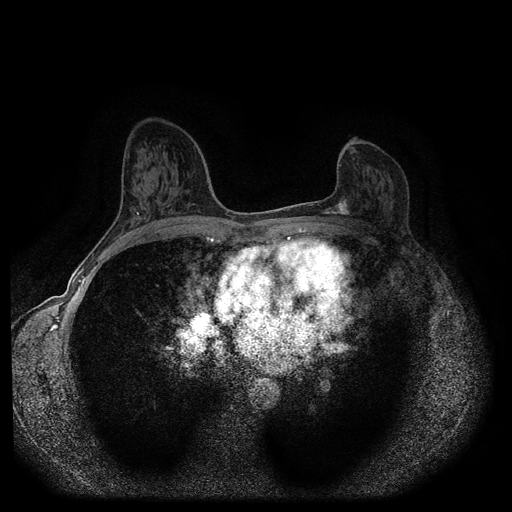
Breast MRI (dynamic contrast-enhanced, multi-phase), one axial slice. Slice 54 of 116 in the series (ordered by position). Dynamic contrast-enhanced series, time point 2 of 5 at this slice position (early post-contrast). 1.5 T. TE 2.6 ms, TR 5.4 ms. 2 mm slice thickness. 512 × 512 image matrix. Female patient, age 57 years.
Outlined on this slice (semi-automatic segmentation, software-assisted and operator-edited):
- breast lesion (labelled 'tumour' in the annotation; benign lesions carry a separate 'benign' label): box from (x=324, y=199) to (x=352, y=217) px